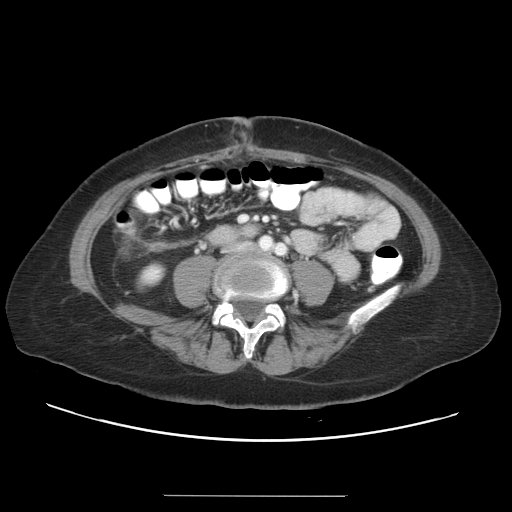
Contrast-enhanced abdominal CT, one axial slice; slice 1 of 34 in the series (ordered by position); reconstruction kernel STANDARD; 120 kVp; intravenous contrast given; soft-tissue window (W 400 / L 40 HU); 512 × 512 image matrix. Female patient, age 69 years. Case-level facts recorded for this patient, not image findings: diagnosis: colorectal cancer liver metastases, imaged before liver resection; multiple liver metastases: yes; largest metastasis: 1.4 cm.
Outlined on this slice (expert manual segmentation):
- portal vein (with intrahepatic branches): box from (x=240, y=216) to (x=246, y=221) px